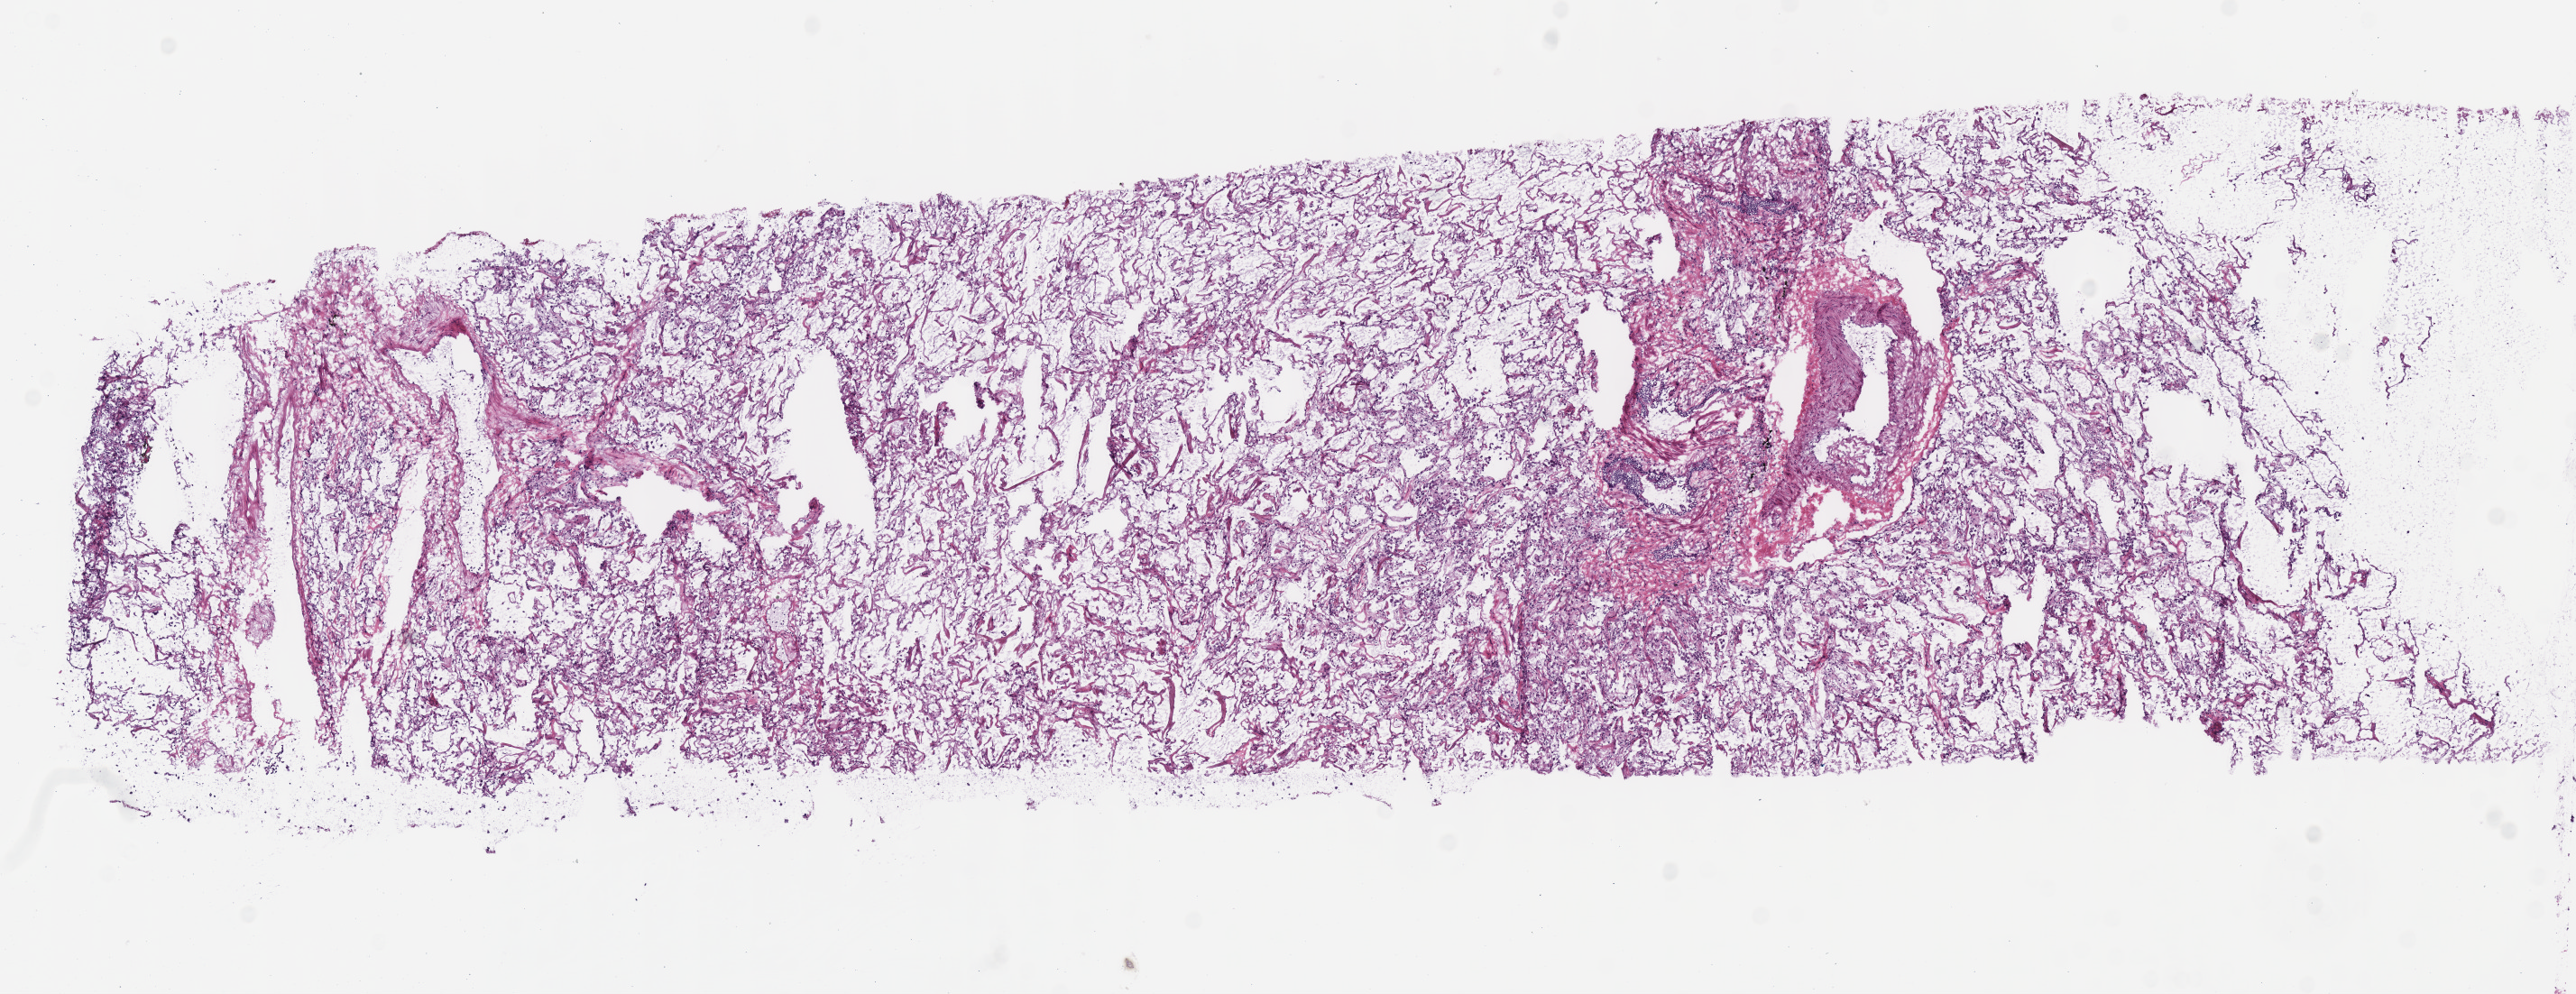
Hematoxylin and eosin (H&E) stained whole-slide image — a low-resolution overview of the entire scanned area, about 11.3 x 4.3 mm (acquisition: 40x scan). Frozen section from the top of the tissue portion. Solid tissue normal (non-tumour tissue) sample from the lung. Patient: male, age at initial diagnosis 76 years.
This section: solid tissue normal (non-tumour) sample from the same patient. Patient diagnosis: Adenocarcinoma, NOS (upper lobe, lung).